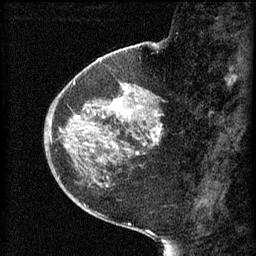
Breast MRI (dynamic contrast-enhanced), one sagittal slice; slice 21 of 60 in the series (ordered by position); 3 images stored at this slice position (order not interpretable as contrast timing); 1.5 T; TE 4.2 ms, TR 8.2 ms; 2 mm slice thickness; 256 × 256 image matrix. Patient: female, 44 years.
Annotated regions visible in this slice (semi-automatic segmentation, software-assisted and operator-edited):
- analysis volume of interest (the breast-tissue region the enhancement analysis was run in; not a lesion): bounding box (x1, y1, x2, y2) in pixels: (73, 82, 165, 165)
- tumour enhancement mask (voxels above the 70 % enhancement threshold inside the analysis volume of interest): (74, 82, 163, 155)